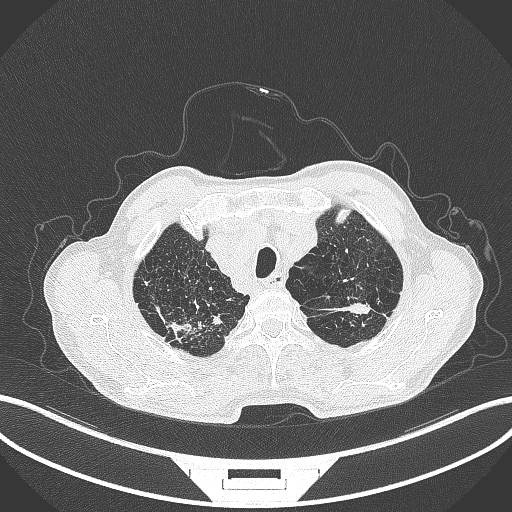
Chest CT, one axial slice. Slice 384 of 463 in the series (ordered by position). Reconstruction kernel B70f. Lung window (W 1500 / L -600 HU). 1 mm slice thickness. 512 × 512 image matrix, field of view 400 × 400 mm. Male patient, age 74 years. Case-level facts recorded for this patient, not image findings: clinical TNM (as recorded): T2a N1 M0.
Annotated regions visible in this slice (bounding box drawn by a radiologist):
- lung tumour (recorded histology: adenocarcinoma): bounding box [x1, y1, x2, y2] px = [335, 296, 378, 319]